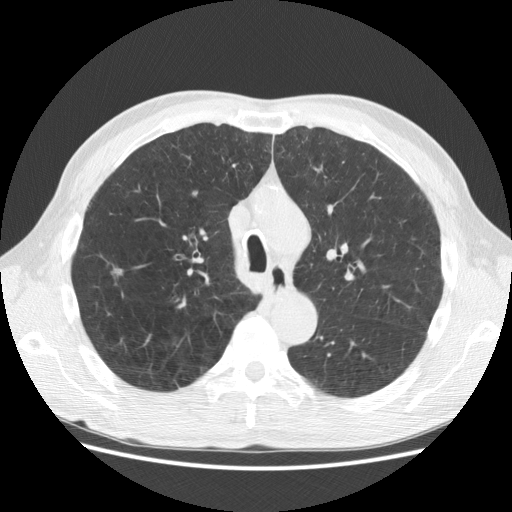
Low-dose screening chest CT, one axial slice. Position 202 of 282 along the scan axis. Reconstruction kernel STANDARD. 120 kVp. Lung window (W 1500 / L -600 HU). 512 × 512 image matrix.
Structures marked on this image (expert manual segmentation):
- lesion 1 (tumor, upper lobe of right lung): bounding box (x1, y1, x2, y2) in pixels: (115, 269, 122, 274)